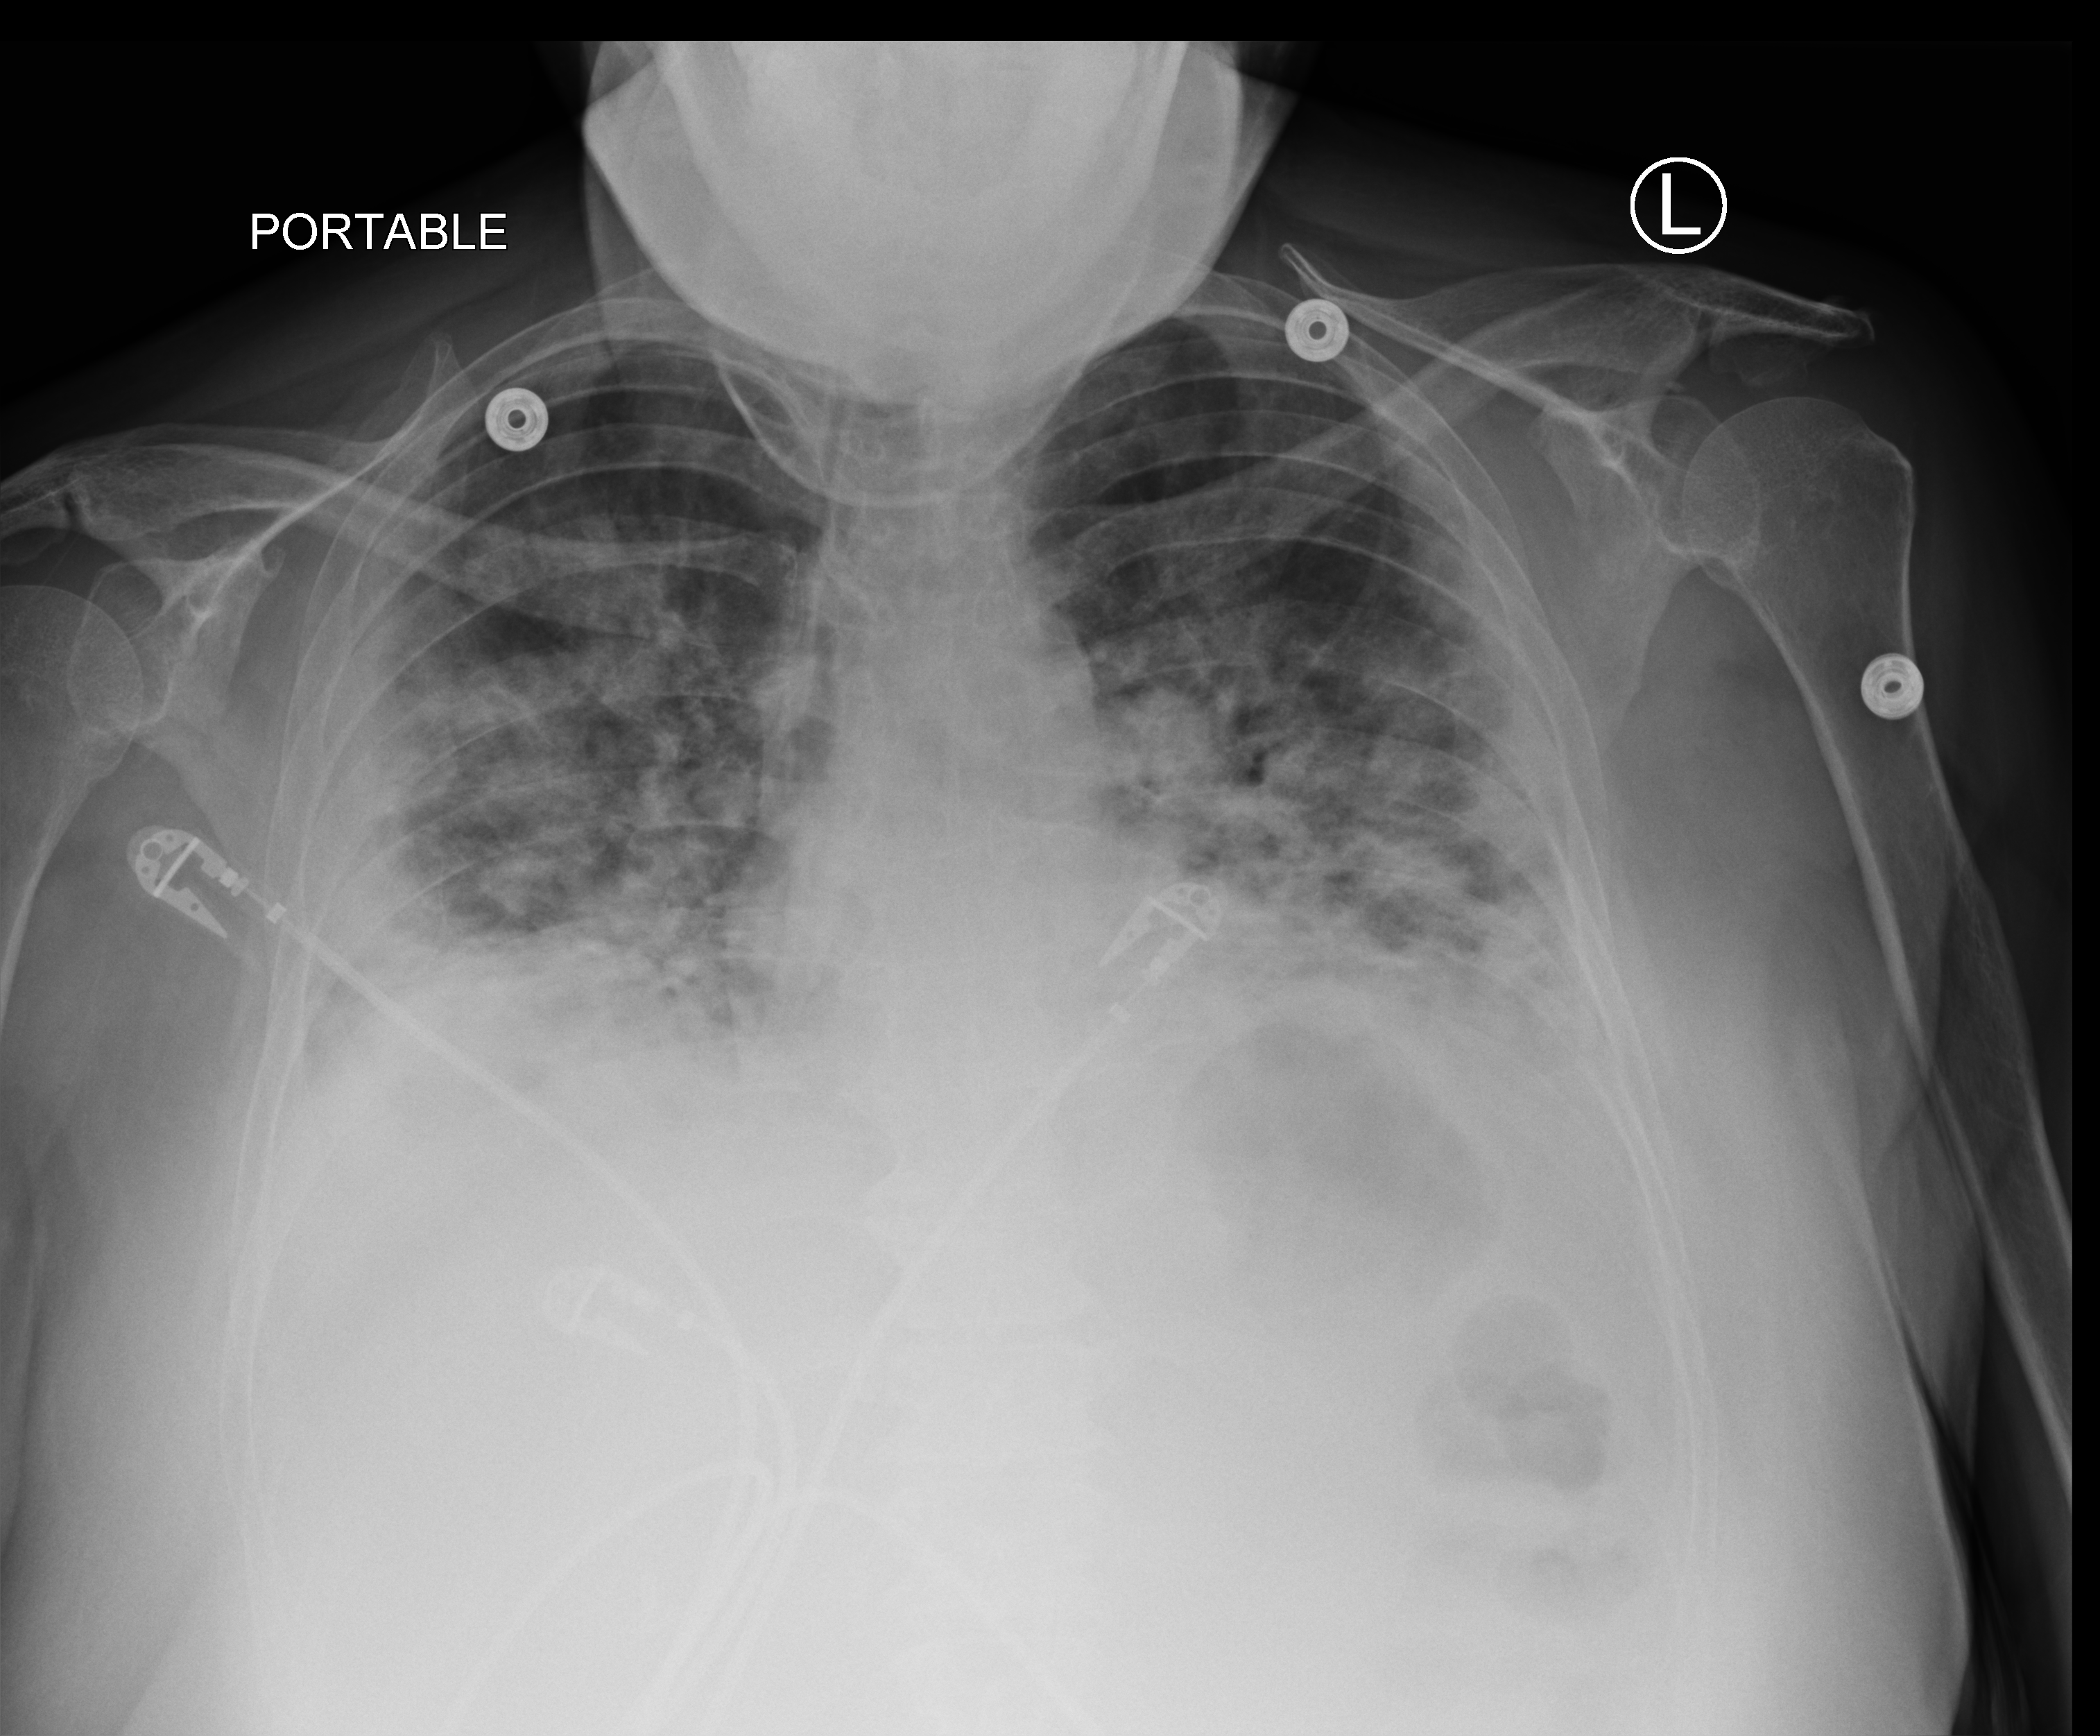
Portable chest radiograph; anteroposterior (AP) projection. Patient hospitalised with COVID-19; female, aged 18–59 years.
From the hospital-stay record, not from the radiograph (when in the stay this image was taken is not recorded):
- admitted to intensive care during this hospital stay: yes
- COPD (admission record): no
- mechanically ventilated during this hospital stay: no